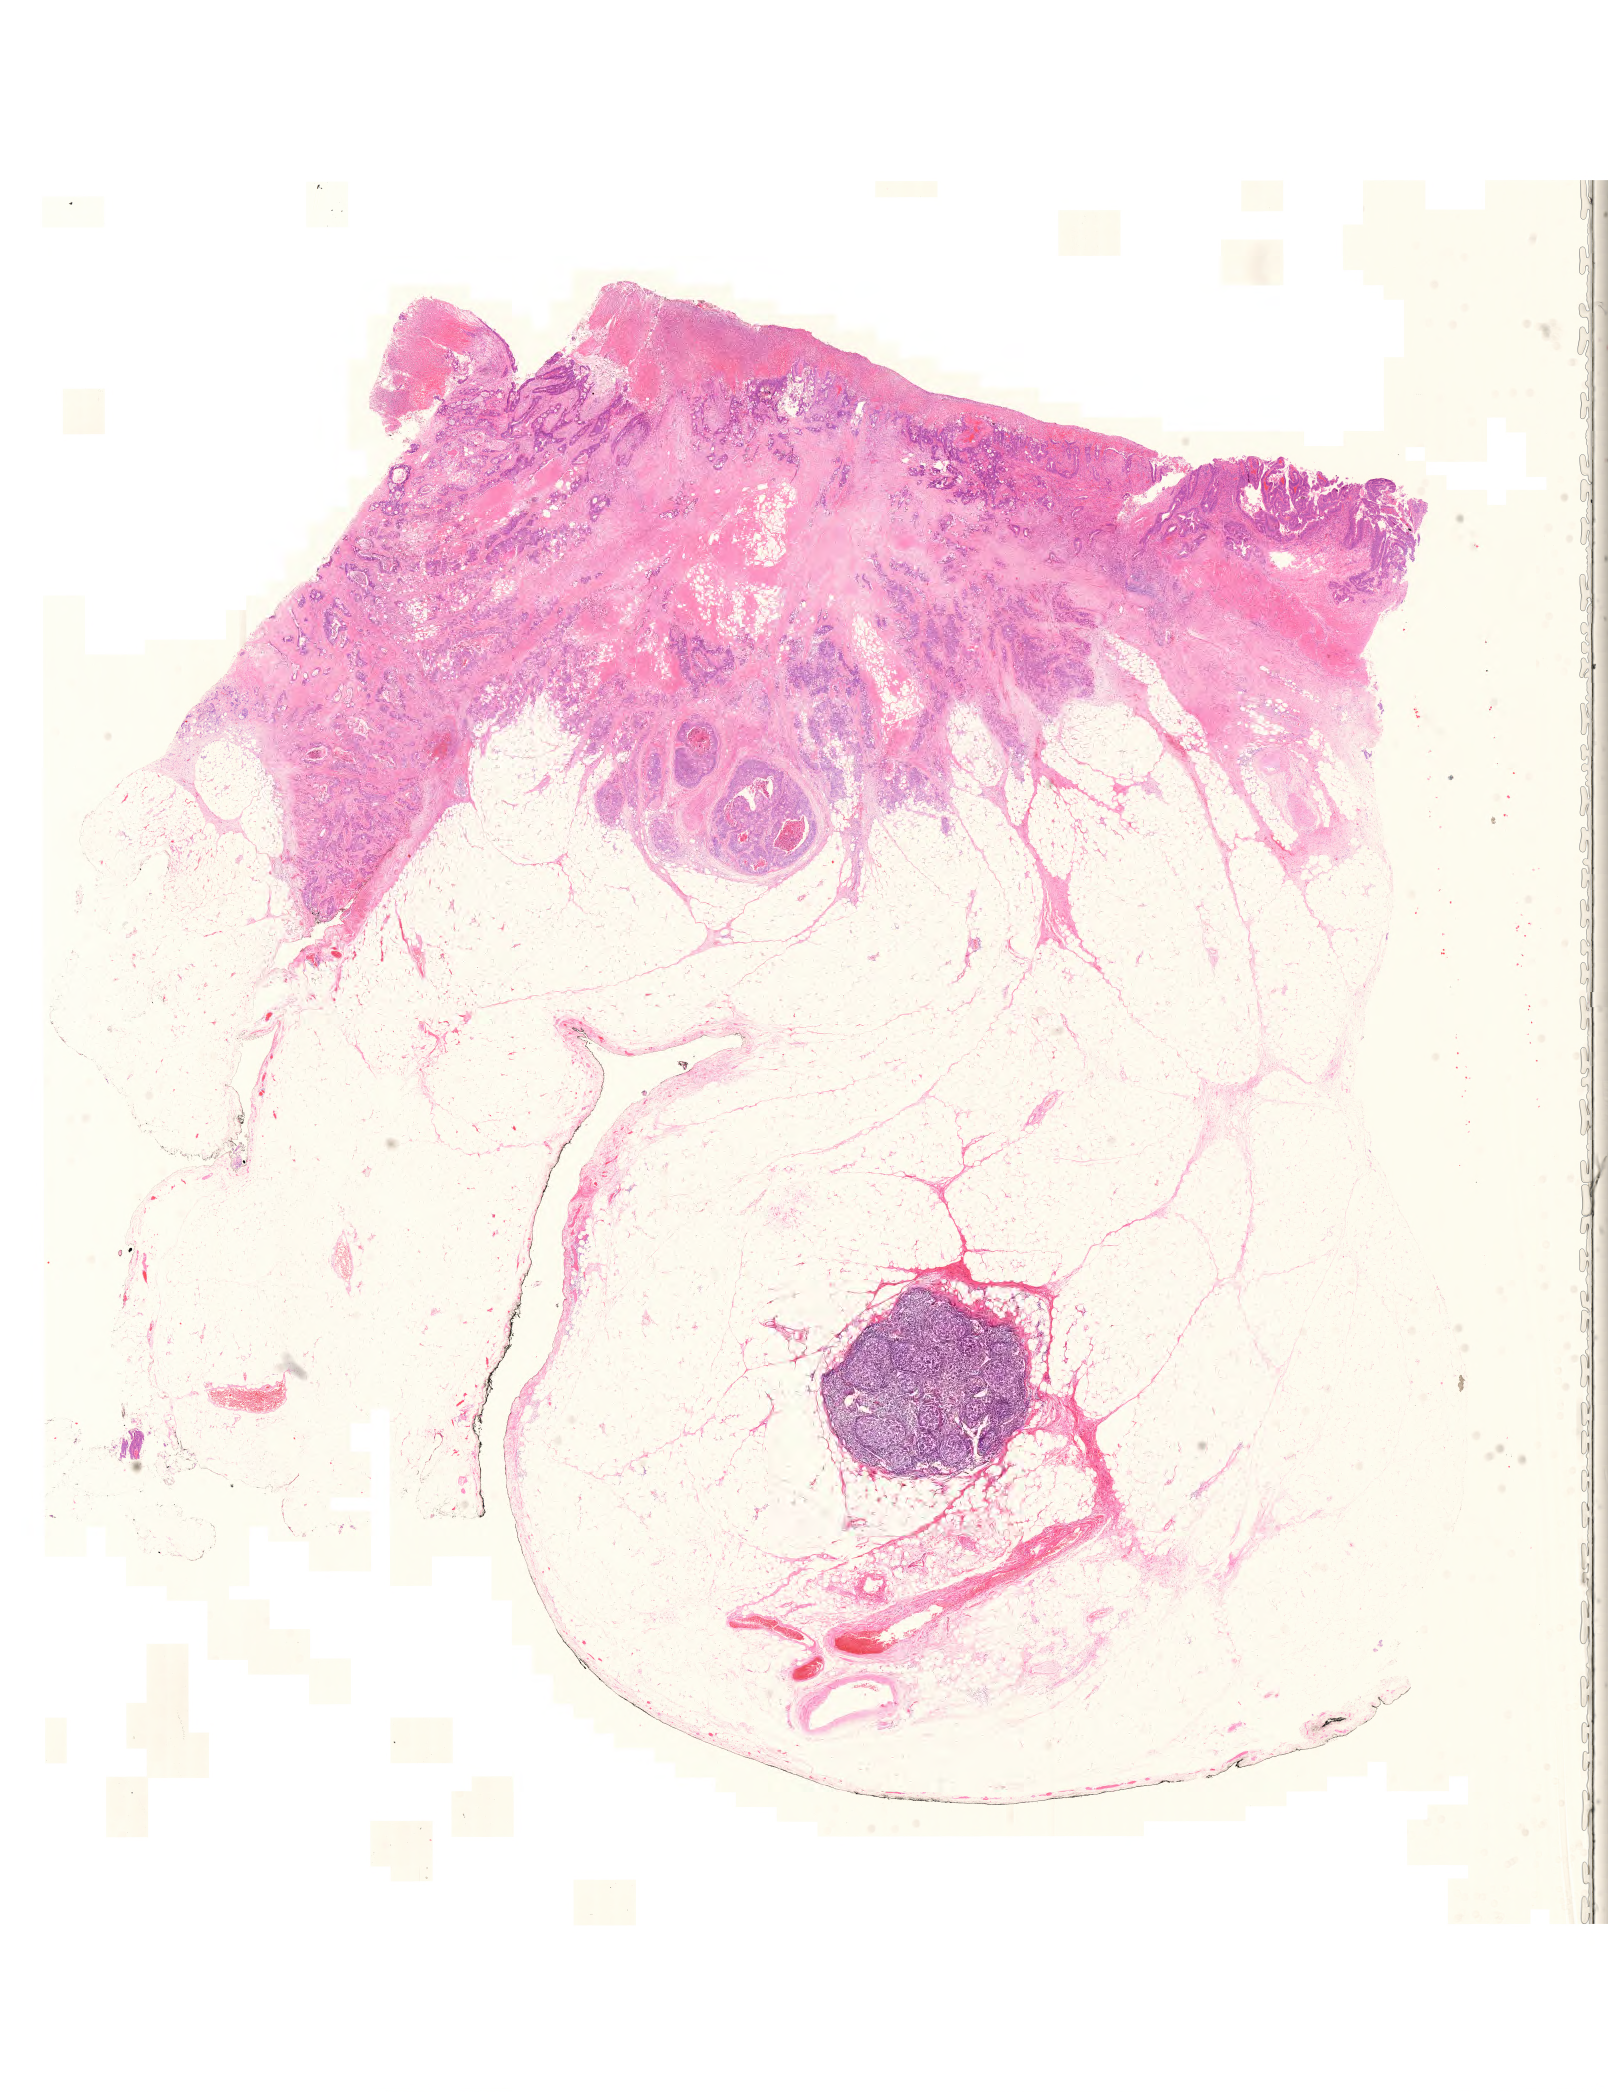
Digitized H&E-stained tissue section (whole slide) — low-resolution overview of the scanned area, about 23.9 x 31.1 mm (slide scanned at 20x). Formalin-fixed paraffin-embedded (FFPE) diagnostic section. Primary tumour sample from the uterus. Patient: female, age at initial diagnosis 54 years. Histologic grade: G1 (well differentiated).
FIGO stage: I. Diagnosis: Endometrioid adenocarcinoma, NOS (endometrium).